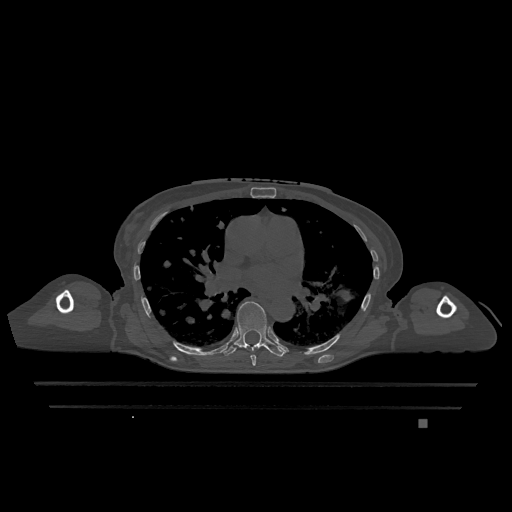
CT including the spine, one axial slice. Position 754 of 1317 along the scan axis. Bone window (W 1800 / L 400 HU). 0.5 mm slice thickness. 512 × 512 image matrix, field of view 500 × 500 mm. Female patient, age 74 years. Case-level facts recorded for this patient, not image findings: primary cancer: lung; vertebrae with lytic lesions (as recorded): T1, T4, T5, T6, L4, L5.
Outlined on this slice (semi-automatically segmented with operator editing):
- T6 vertebra: bounding box <250,354,256,366> (left, top, right, bottom; pixels)
- T7 vertebra: <222,301,286,357>